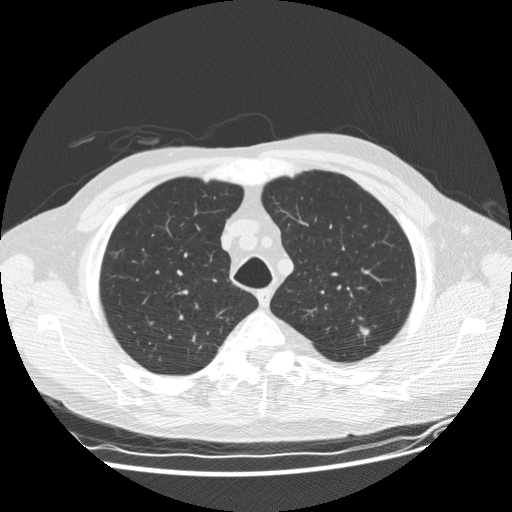
Low-dose screening chest CT, one axial slice; position 145 of 177 along the scan axis; reconstruction kernel STANDARD; lung window (W 1500 / L -600 HU); 2.5 mm slice thickness; 512 × 512 image matrix, field of view 360 × 360 mm.
Structures marked on this image (manually delineated by an expert):
- lesion 1 (tumor, upper lobe of left lung): box from (x=360, y=327) to (x=369, y=336) px